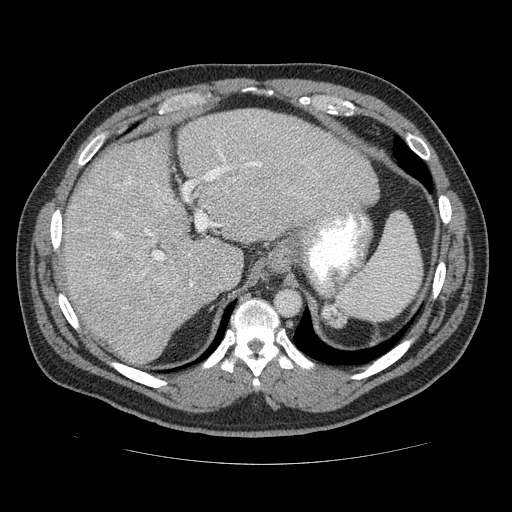
Contrast-enhanced abdominal CT (liver protocol), one axial slice; reconstruction kernel STANDARD; 120 kVp; soft-tissue window (W 400 / L 40 HU); 512 × 512 image matrix, field of view 400 × 400 mm. Case-level facts recorded for this patient, not image findings: diagnosis: hepatocellular carcinoma (patient treated with transarterial chemoembolisation; whether this scan precedes or follows treatment is not stated here); TNM stage (as recorded): Stage-II; Child-Pugh class: B; tumour nodularity: multinodular; tumour size: 4.8 cm.
Outlined on this slice (semi-automatic segmentation, software-assisted and operator-edited):
- liver parenchyma outside the tumour (the mass and vessels are separate outlines, so this box may not span the whole liver): box from (x=54, y=110) to (x=380, y=363) px
- mass: (x=93, y=244)–(x=179, y=303)
- liver vessels: (x=114, y=145)–(x=328, y=304)